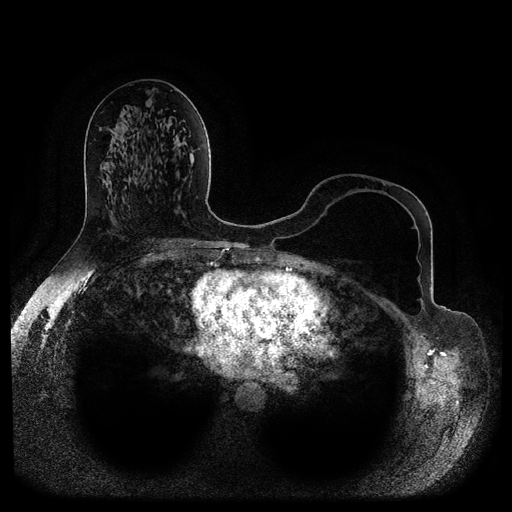
Breast MRI (dynamic contrast-enhanced, multi-phase), one axial slice. Position 49 of 116 along the scan axis. Dynamic contrast-enhanced series, time point 2 of 5 at this slice position (early post-contrast). 1.5 T. TE 2.6 ms, TR 5.2 ms. 2 mm slice thickness. 512 × 512 image matrix, field of view 380 × 380 mm. Female patient, age 56 years.
Annotated regions visible in this slice (semi-automatically segmented with operator editing):
- breast lesion (labelled benign in the annotation): bounding box (x1, y1, x2, y2) in pixels: (160, 123, 165, 137)